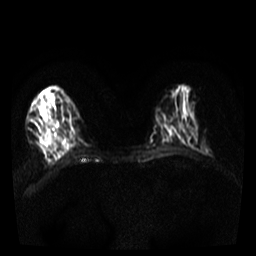
Breast MRI, one axial slice. Position 12 of 36 along the scan axis. Diffusion-weighted series; image 2 of 4 stored at this slice position (different b-values; order by instance number). 3 T. 5 mm slice thickness. 256 × 256 image matrix. Female patient.
Annotated regions visible in this slice (expert manual segmentation):
- tumour on diffusion-weighted imaging: box from (x=41, y=131) to (x=52, y=145) px